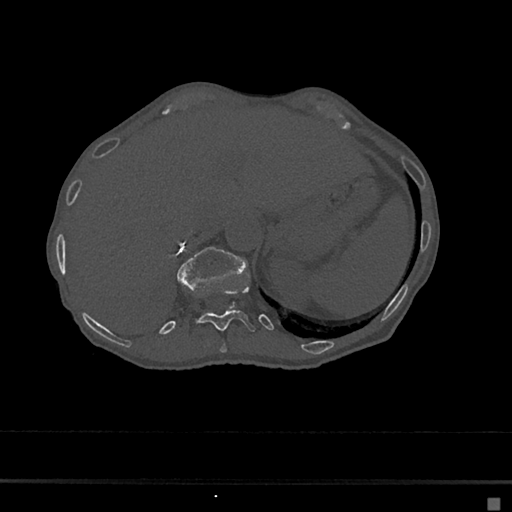
CT including the spine, one axial slice. Position 164 of 797 along the scan axis. 120 kVp. Bone window (W 1800 / L 400 HU). 512 × 512 image matrix, field of view 360 × 360 mm. Patient: female, 68 years. Case-level facts recorded for this patient, not image findings: primary cancer: renal.
Annotated regions visible in this slice (semi-automatic segmentation, software-assisted and operator-edited):
- T10 vertebra: bounding box <220,343,227,354> (left, top, right, bottom; pixels)
- T11 vertebra: <195,284,256,332>
- T12 vertebra: <176,247,248,289>